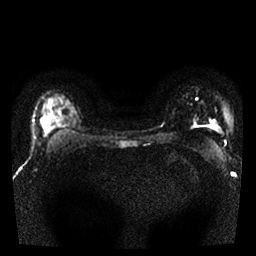
Breast MRI, one axial slice. Slice 19 of 25 in the series (ordered by position). Diffusion-weighted series; image 2 of 4 stored at this slice position (different b-values; order by instance number). 1.5 T. 4 mm slice thickness. 256 × 256 image matrix. Female patient.
Outlined on this slice (expert manual segmentation):
- tumour on diffusion-weighted imaging: bounding box [x1, y1, x2, y2] px = [41, 117, 54, 132]